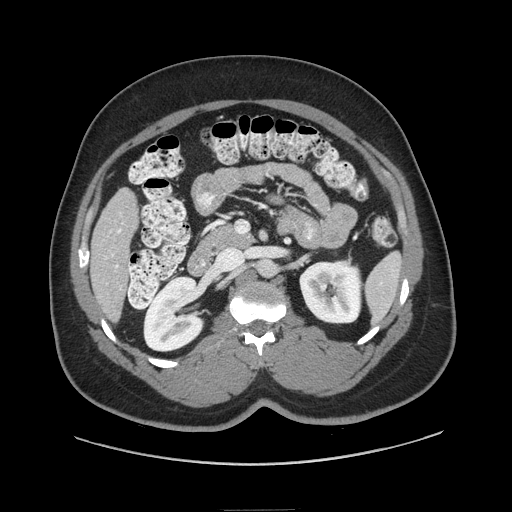
Contrast-enhanced abdominal CT (liver protocol), one axial slice; slice 26 of 87 in the series (ordered by position); soft-tissue window (W 400 / L 40 HU); 512 × 512 image matrix, field of view 440 × 440 mm. From the clinical record (not read from this slice): diagnosis: hepatocellular carcinoma (patient treated with transarterial chemoembolisation; whether this scan precedes or follows treatment is not stated here); TNM stage (as recorded): Stage-II.
Annotated regions visible in this slice (semi-automatic segmentation, software-assisted and operator-edited):
- liver parenchyma outside the tumour (the mass and vessels are separate outlines, so this box may not span the whole liver): bounding box (x1, y1, x2, y2) in pixels: (90, 188, 138, 320)
- liver vessels: (105, 229, 121, 268)